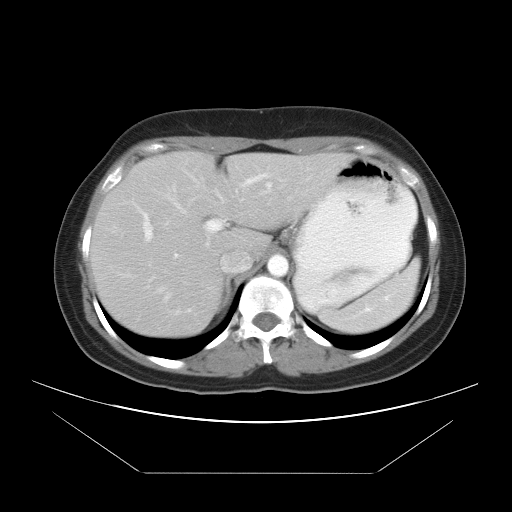
Contrast-enhanced abdominal CT, one axial slice. Position 27 of 34 along the scan axis. Reconstruction kernel STANDARD. 120 kVp. Intravenous contrast given. Soft-tissue window (W 400 / L 40 HU). 512 × 512 image matrix, field of view 410 × 410 mm. Female patient, age 38 years. Case-level facts recorded for this patient, not image findings: diagnosis: colorectal cancer liver metastases, imaged before liver resection; multiple liver metastases: yes; largest metastasis: 3.1 cm; disease in both lobes: no.
Annotated regions visible in this slice (outlined manually by an expert reader):
- hepatic veins: bounding box [x1, y1, x2, y2] px = [159, 183, 272, 291]
- liver: [92, 152, 352, 338]
- planned liver remnant (the part of the liver to remain after resection): [199, 153, 352, 256]
- portal vein (with intrahepatic branches): [144, 175, 265, 239]